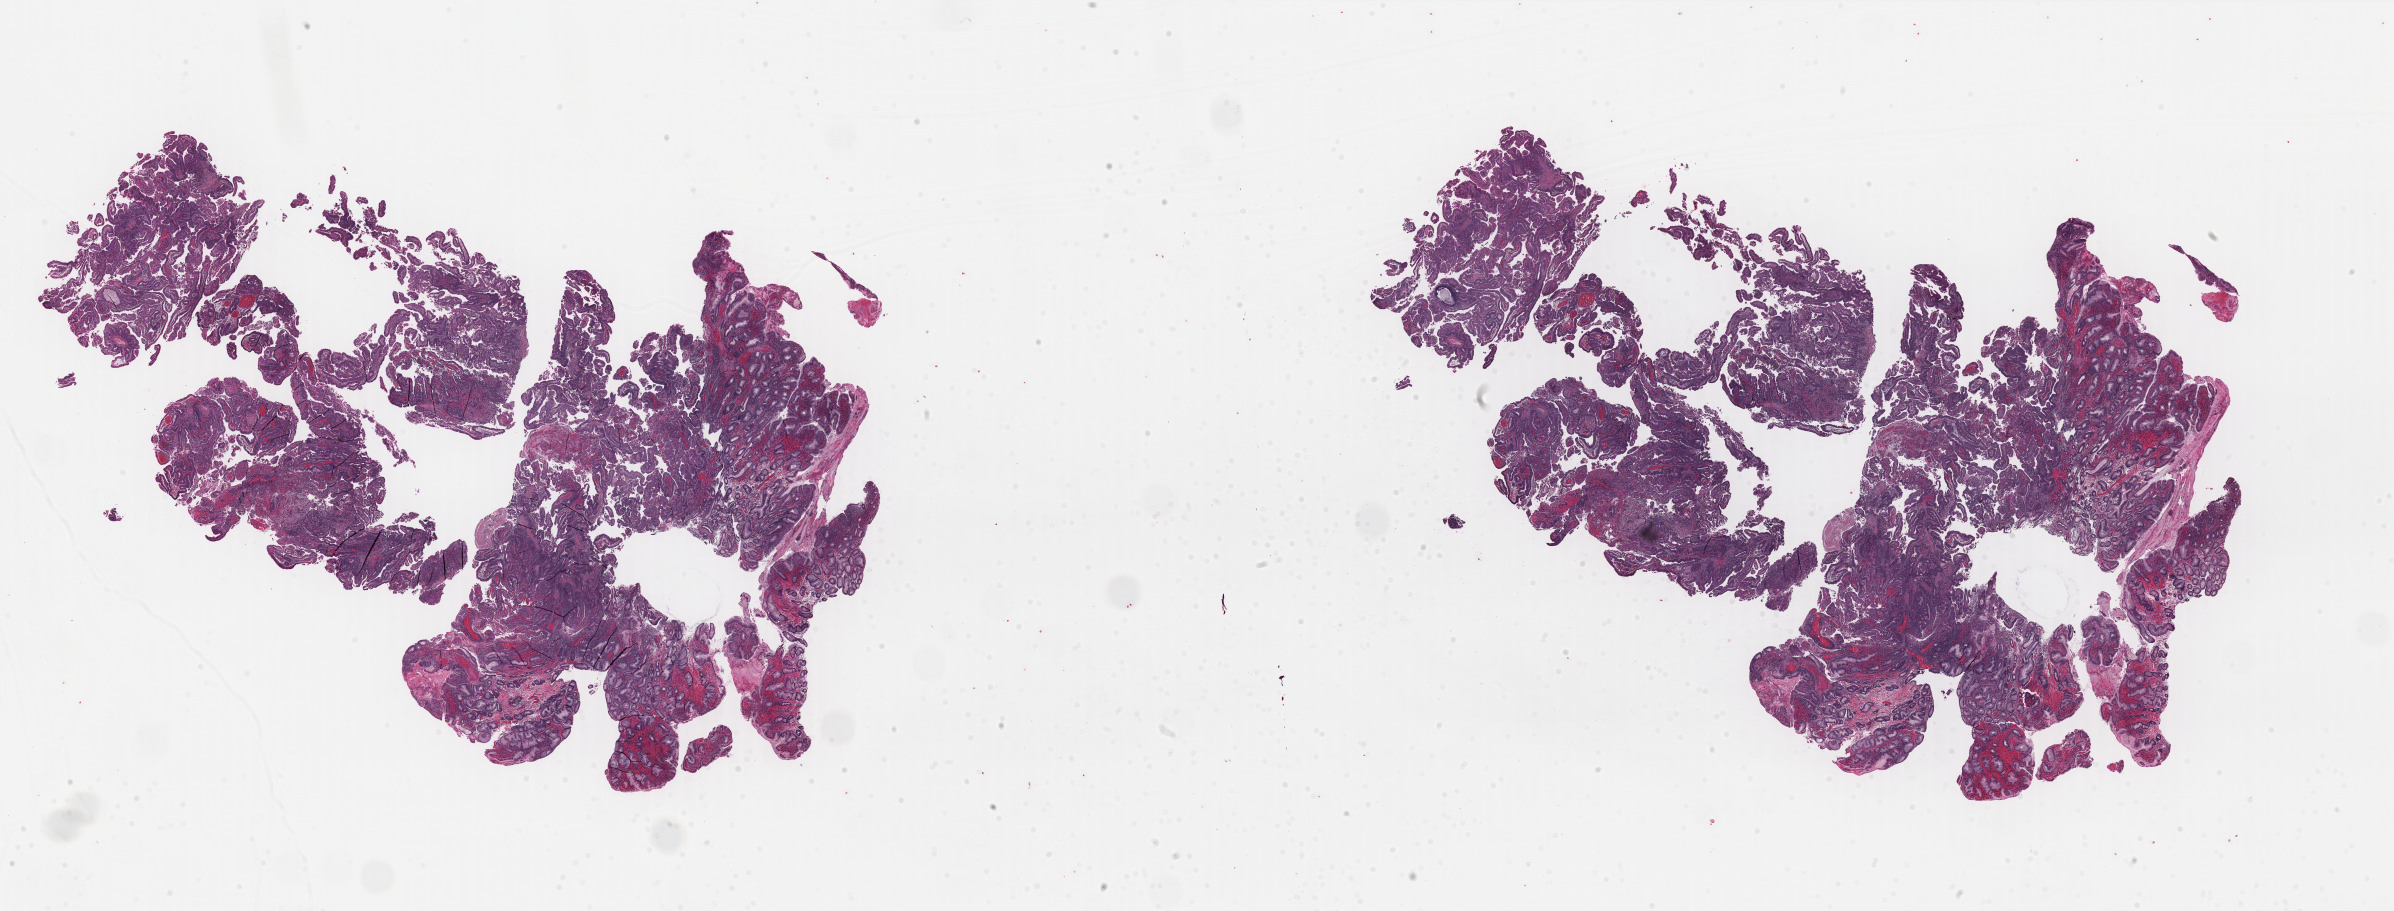
Digitized Hematoxylin and eosin (H&E) stained tissue section (whole slide), low-resolution overview of the scanned area, about 37.9 x 14.4 mm (from a 40x scan), formalin-fixed paraffin-embedded (FFPE) diagnostic section, stomach, primary tumour sample. Male patient; age at initial diagnosis 68 years. Histologic grade: G2 (moderately differentiated).
AJCC pathologic stage: IIA. Histologic diagnosis: Adenocarcinoma, intestinal type. Lymph nodes positive (case pathology): 0 of 13 examined.